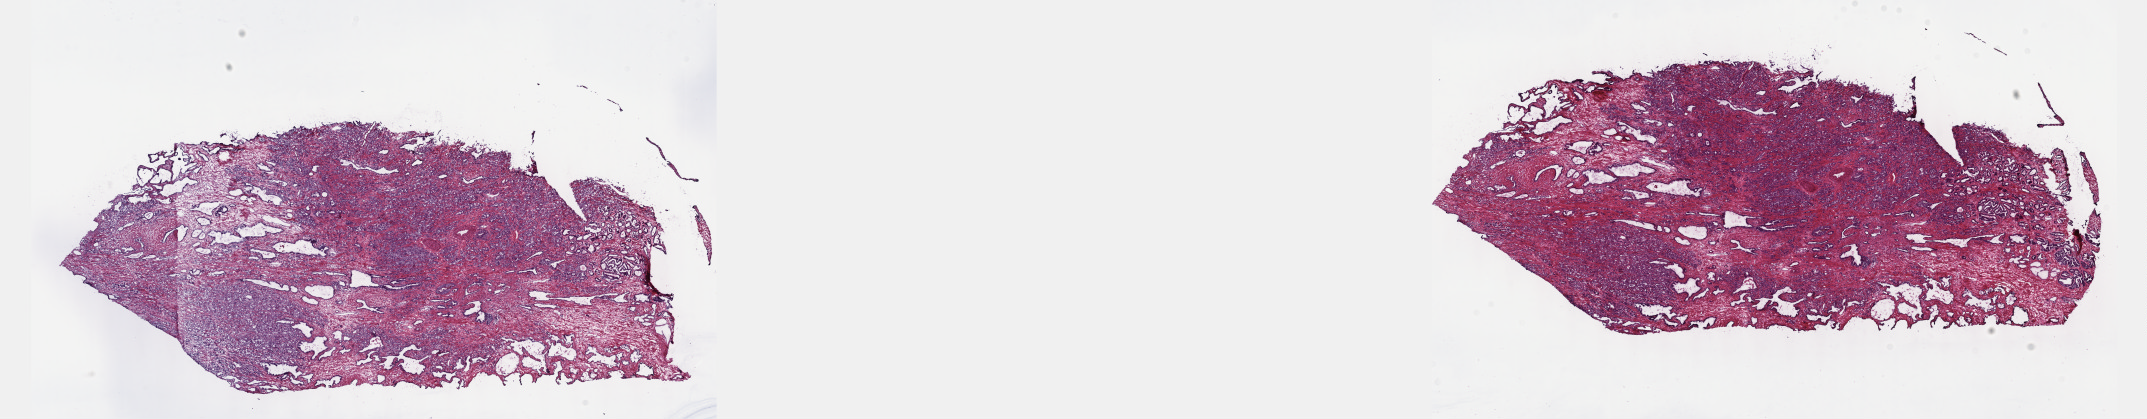
Whole-slide histology image, Hematoxylin and eosin (H&E) stained, low-resolution overview of the scanned area, about 34.7 x 6.8 mm (slide scanned at 40x), frozen section from the top of the tissue portion, prostate, primary tumour sample. Male, age 68 years at initial diagnosis. Gleason score: 8 (4+4). Slide review estimates, as recorded: tumour cells 44%, tumour nuclei 90%, normal cells 10%, stromal cells 45%, necrosis 1%. Infiltration values recorded for this section: lymphocyte infiltration 8%, monocyte infiltration 0%, neutrophil infiltration 0%.
* laterality: left
* lymph nodes positive (case pathology): 0 of 6 examined
* histologic diagnosis: Signet ring cell carcinoma (prostate gland)